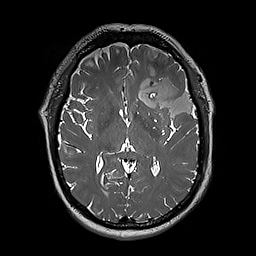
Brain MRI from a brain-tumour surgery series, one axial slice; slice 110 of 192 in the series (ordered by position); 256 × 256 image matrix, field of view 250 × 250 mm. Case-level facts recorded for this patient, not image findings: histopathology: Oligodendroglioma; WHO grade: 3; IDH mutation: yes.
Structures marked on this image (manually delineated by an expert):
- tumour: bounding box [x1, y1, x2, y2] px = [124, 65, 197, 121]